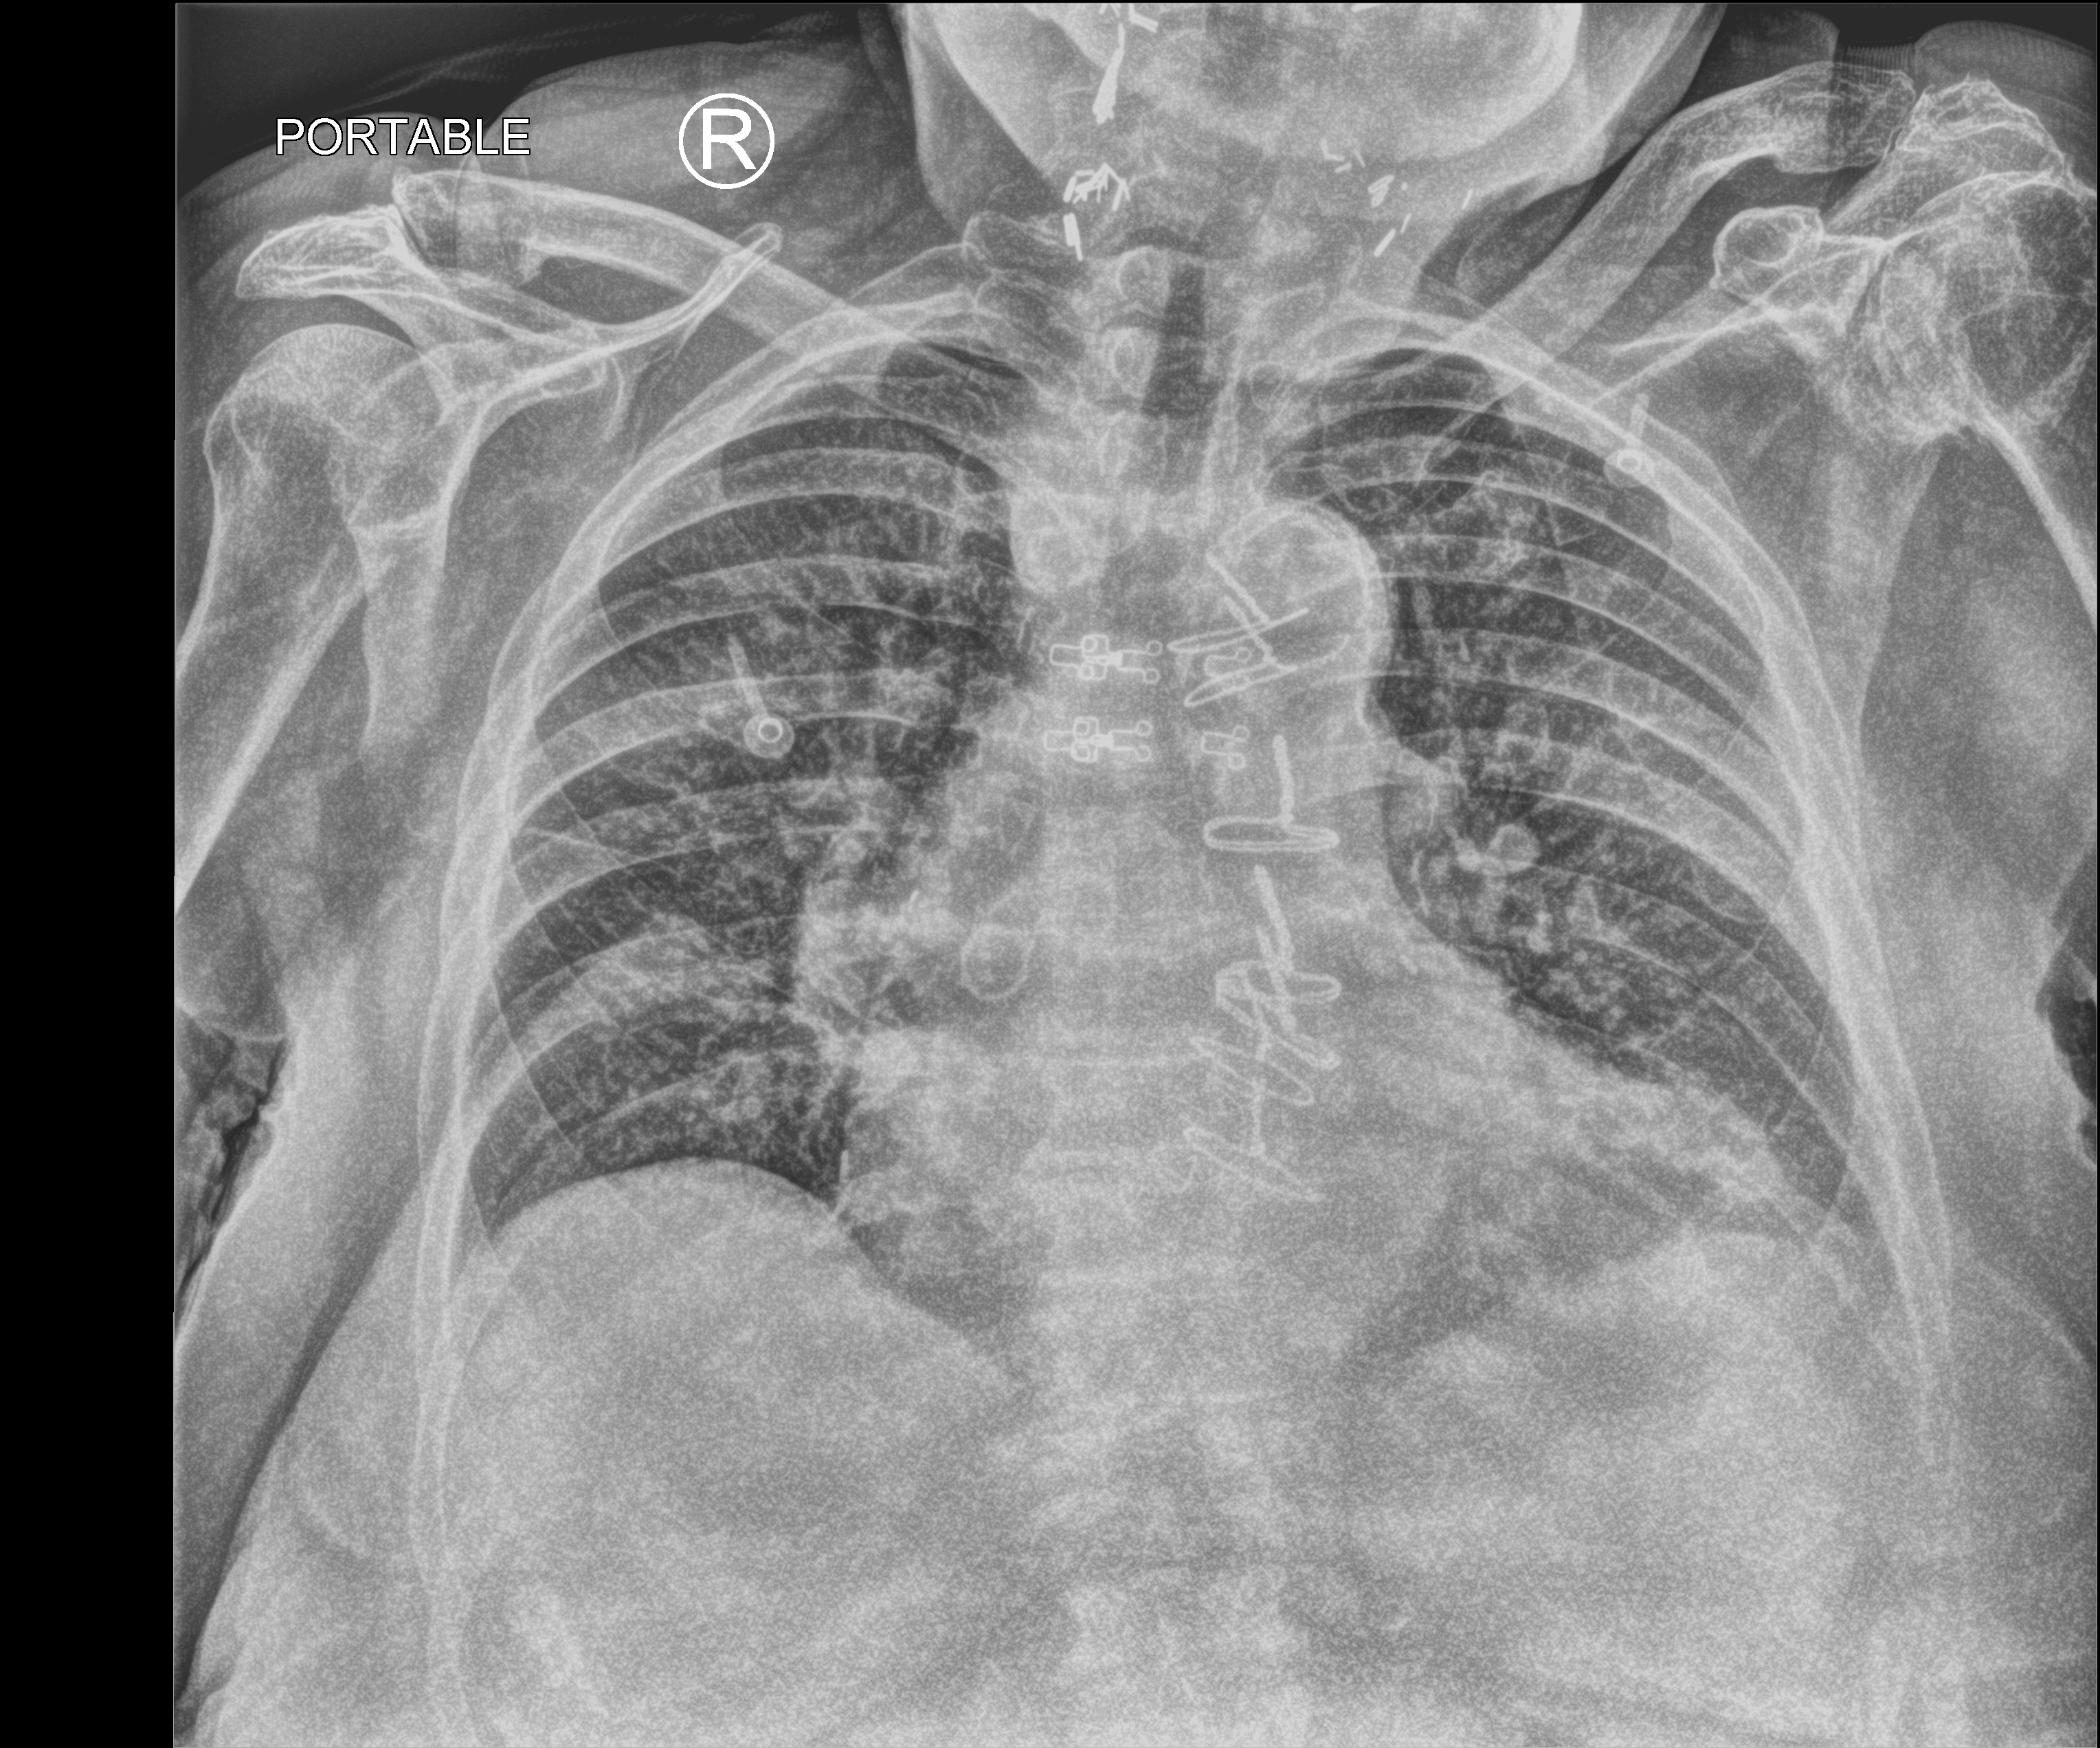
Chest X-ray (portable), anteroposterior (AP) projection. Patient hospitalised with COVID-19; female, aged 75–90 years.
Hospital-stay facts (about this admission, not read from this image; timing relative to this image not recorded): admitted to intensive care during this hospital stay: no.